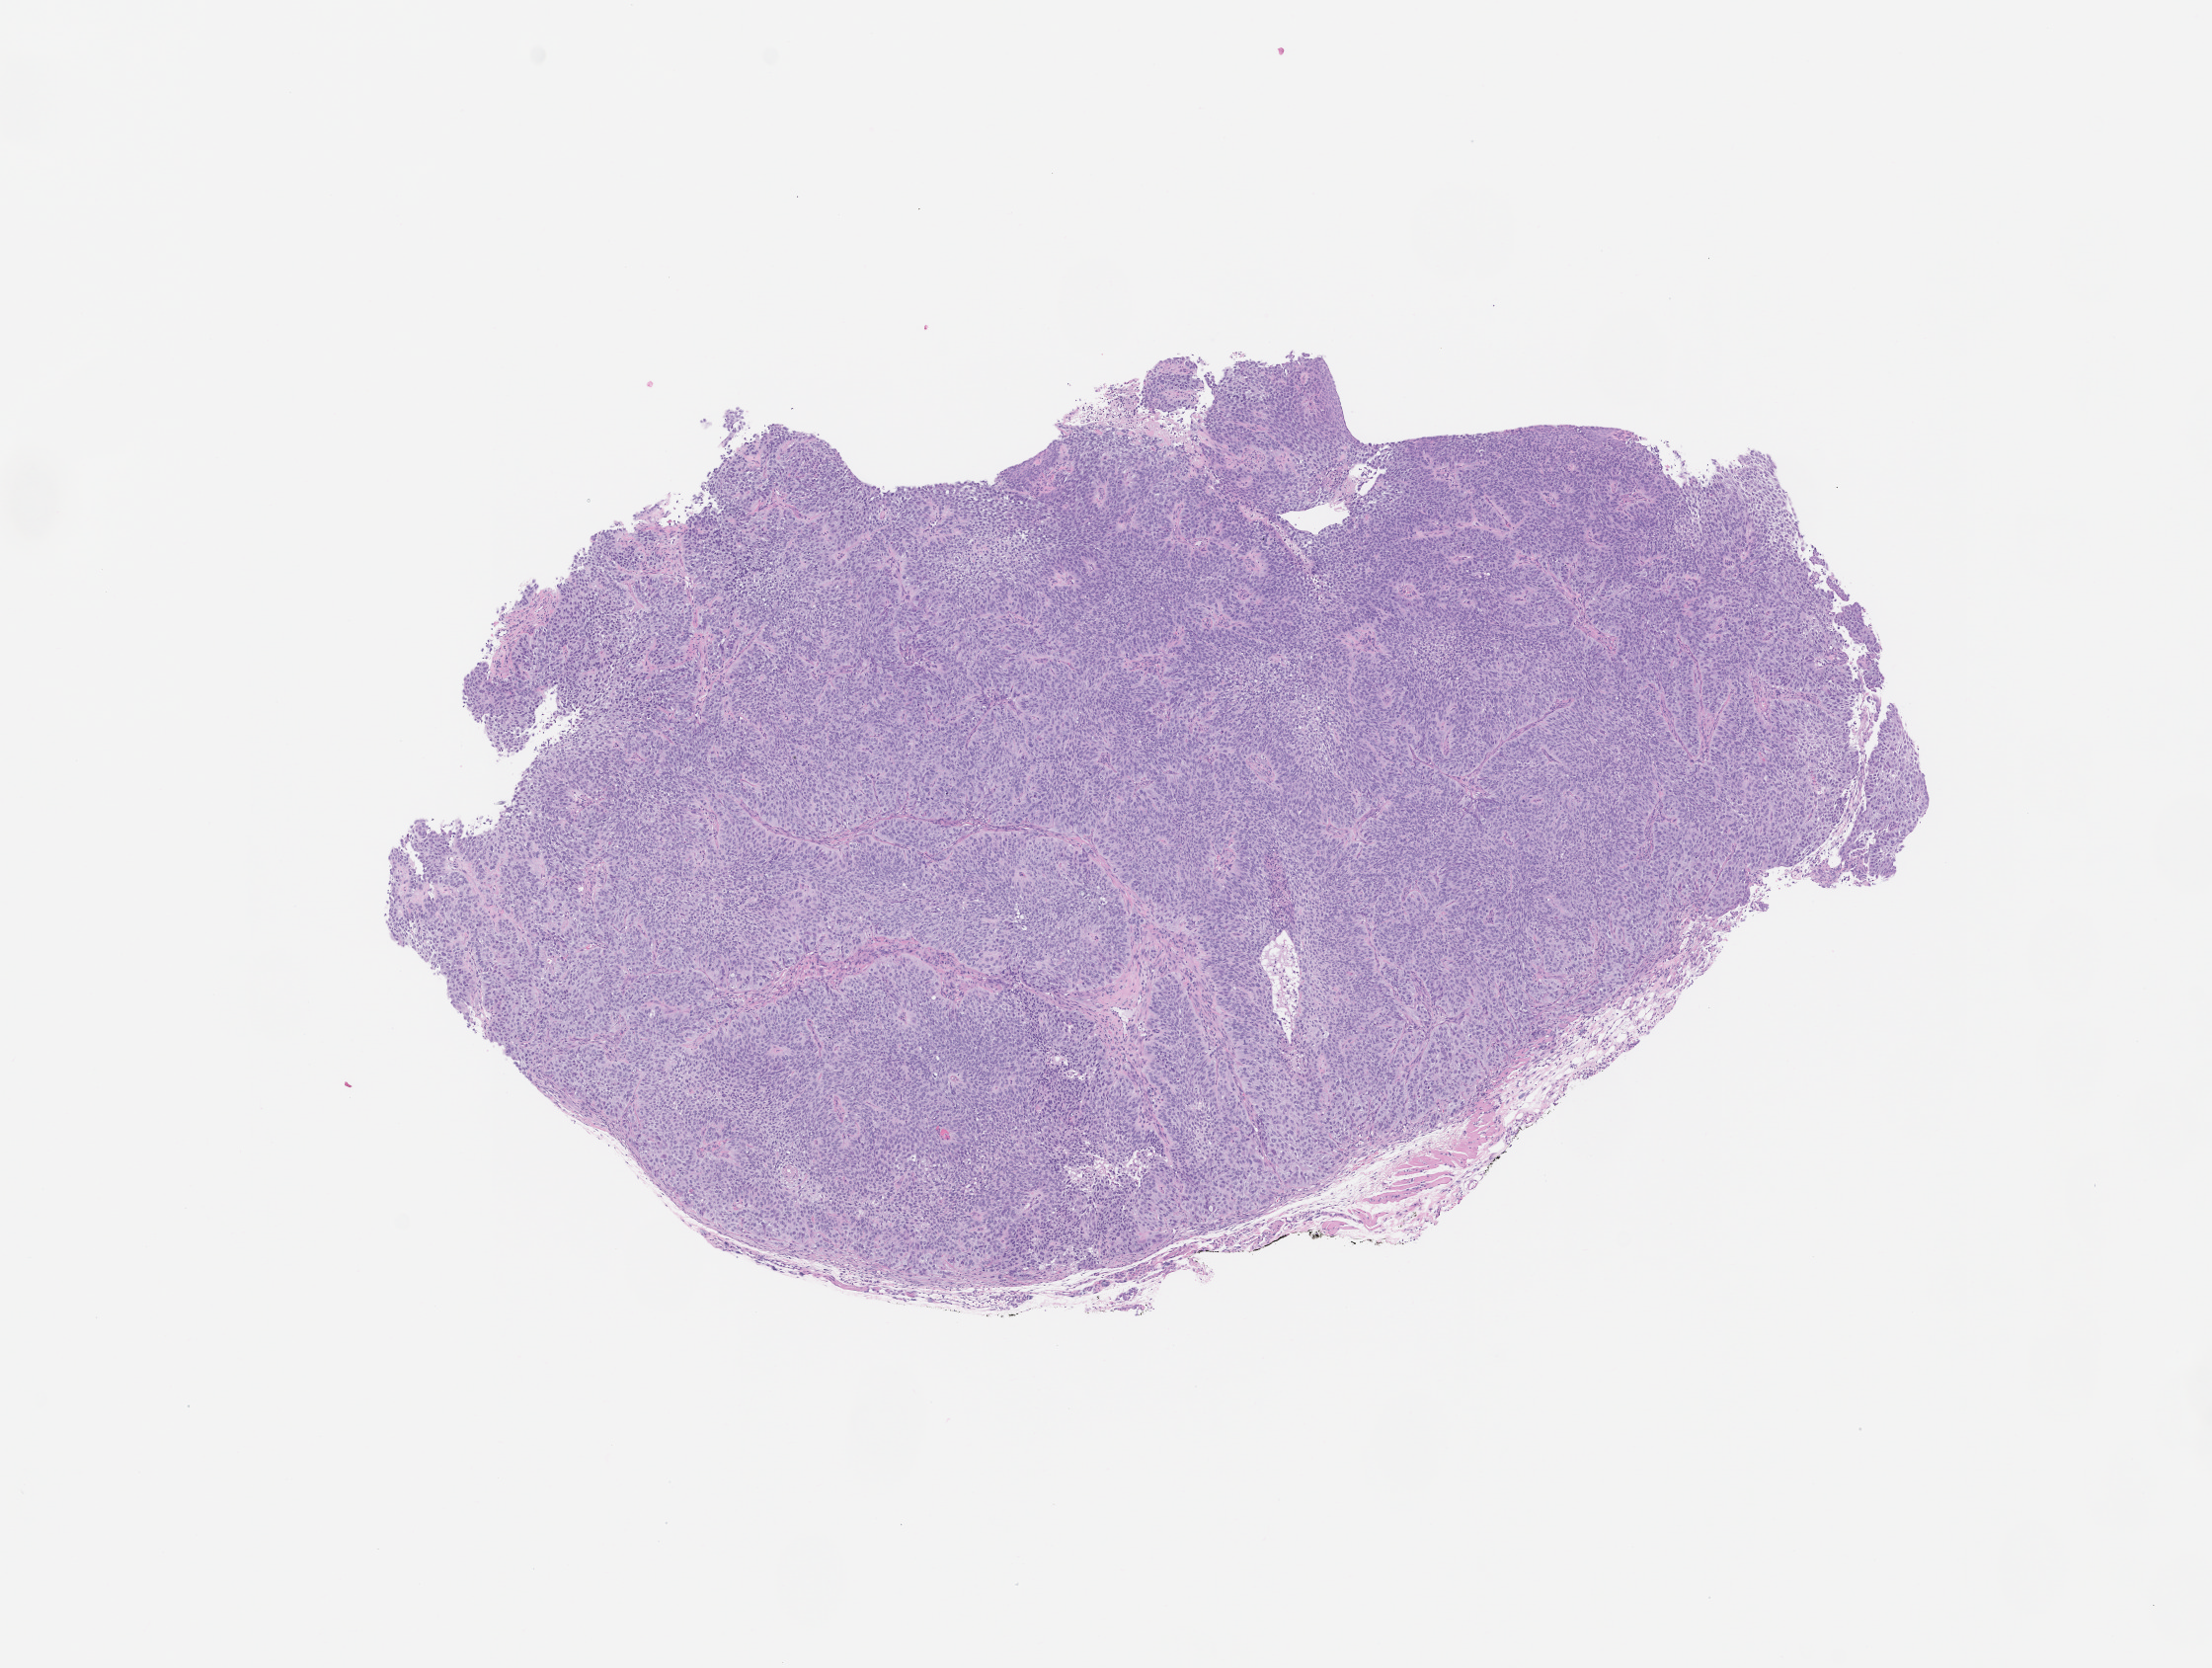
Whole-slide image, hematoxylin and eosin (H&E): patient-derived xenograft (human tumor grown in a mouse), passage 1, a low-resolution overview of the entire scanned area, about 9.0 x 6.8 mm, formalin-fixed, paraffin-embedded (FFPE) tissue, tumor site category: lung.
Originating patient diagnosis: Lung Squamous Cell Carcinoma.